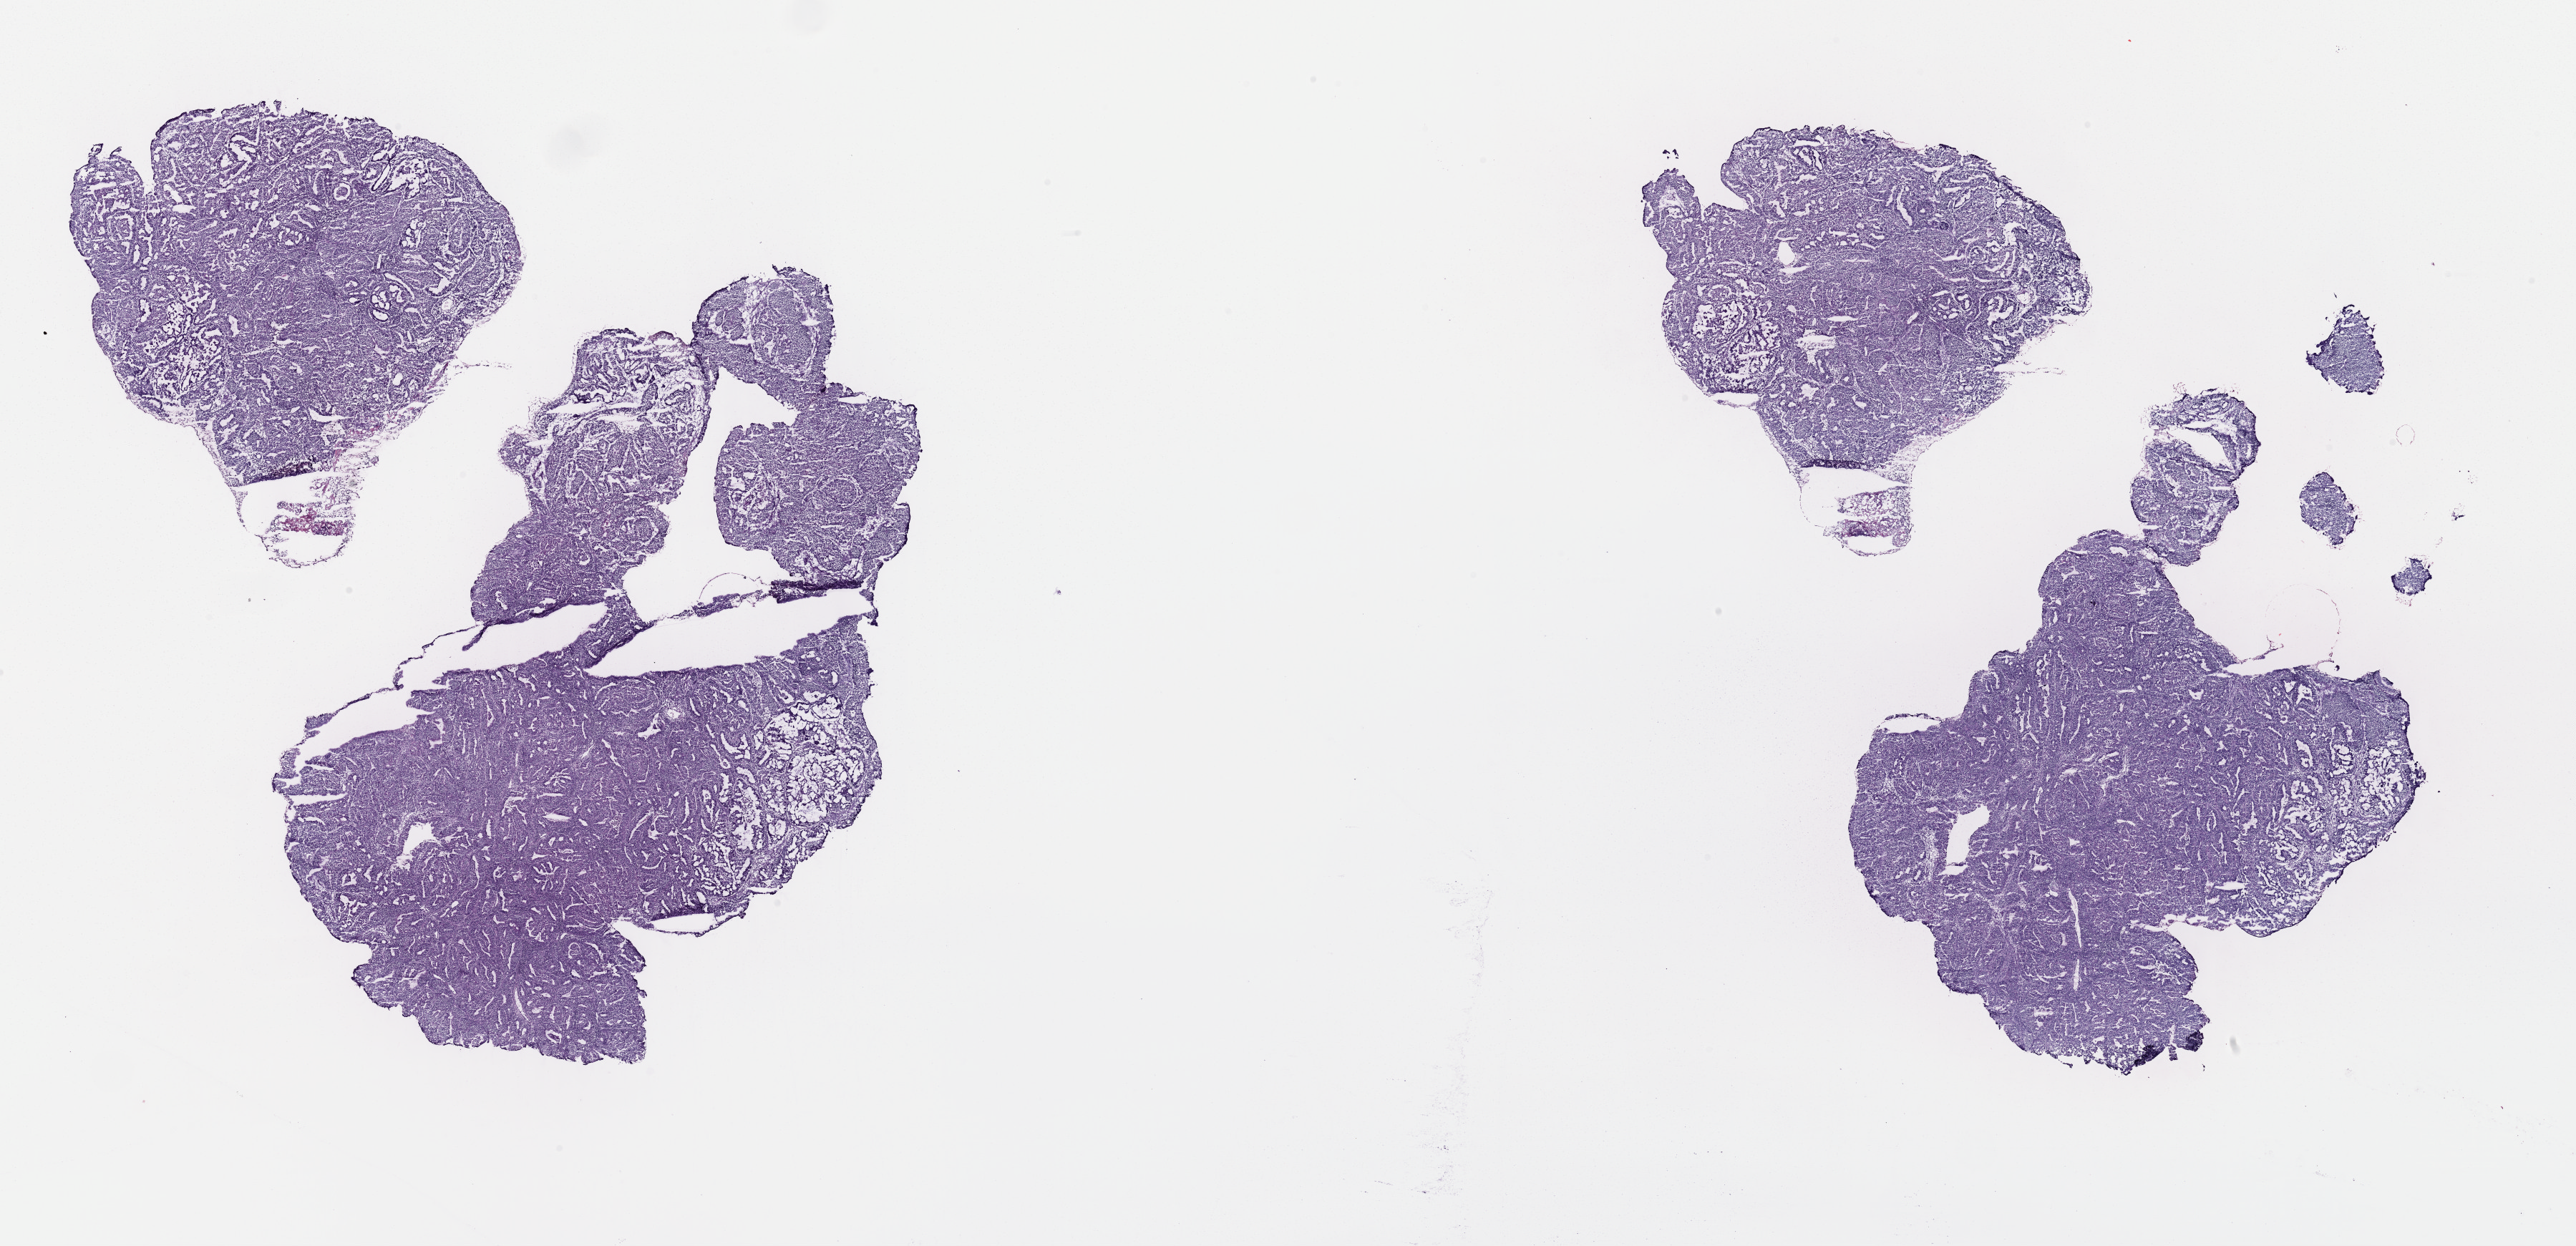
Whole-slide histology image, H&E, low-resolution overview of the scanned area, about 28.4 x 13.8 mm (acquisition: 40x scan); formalin-fixed paraffin-embedded (FFPE) diagnostic section; primary tumour sample from the uterus. Female patient; age at initial diagnosis 57 years. Histologic grade: G2 (moderately differentiated).
Lymph nodes positive (case pathology): 3 of 8 examined. FIGO stage: IIIC2. Pathologic diagnosis: Endometrioid adenocarcinoma, NOS.